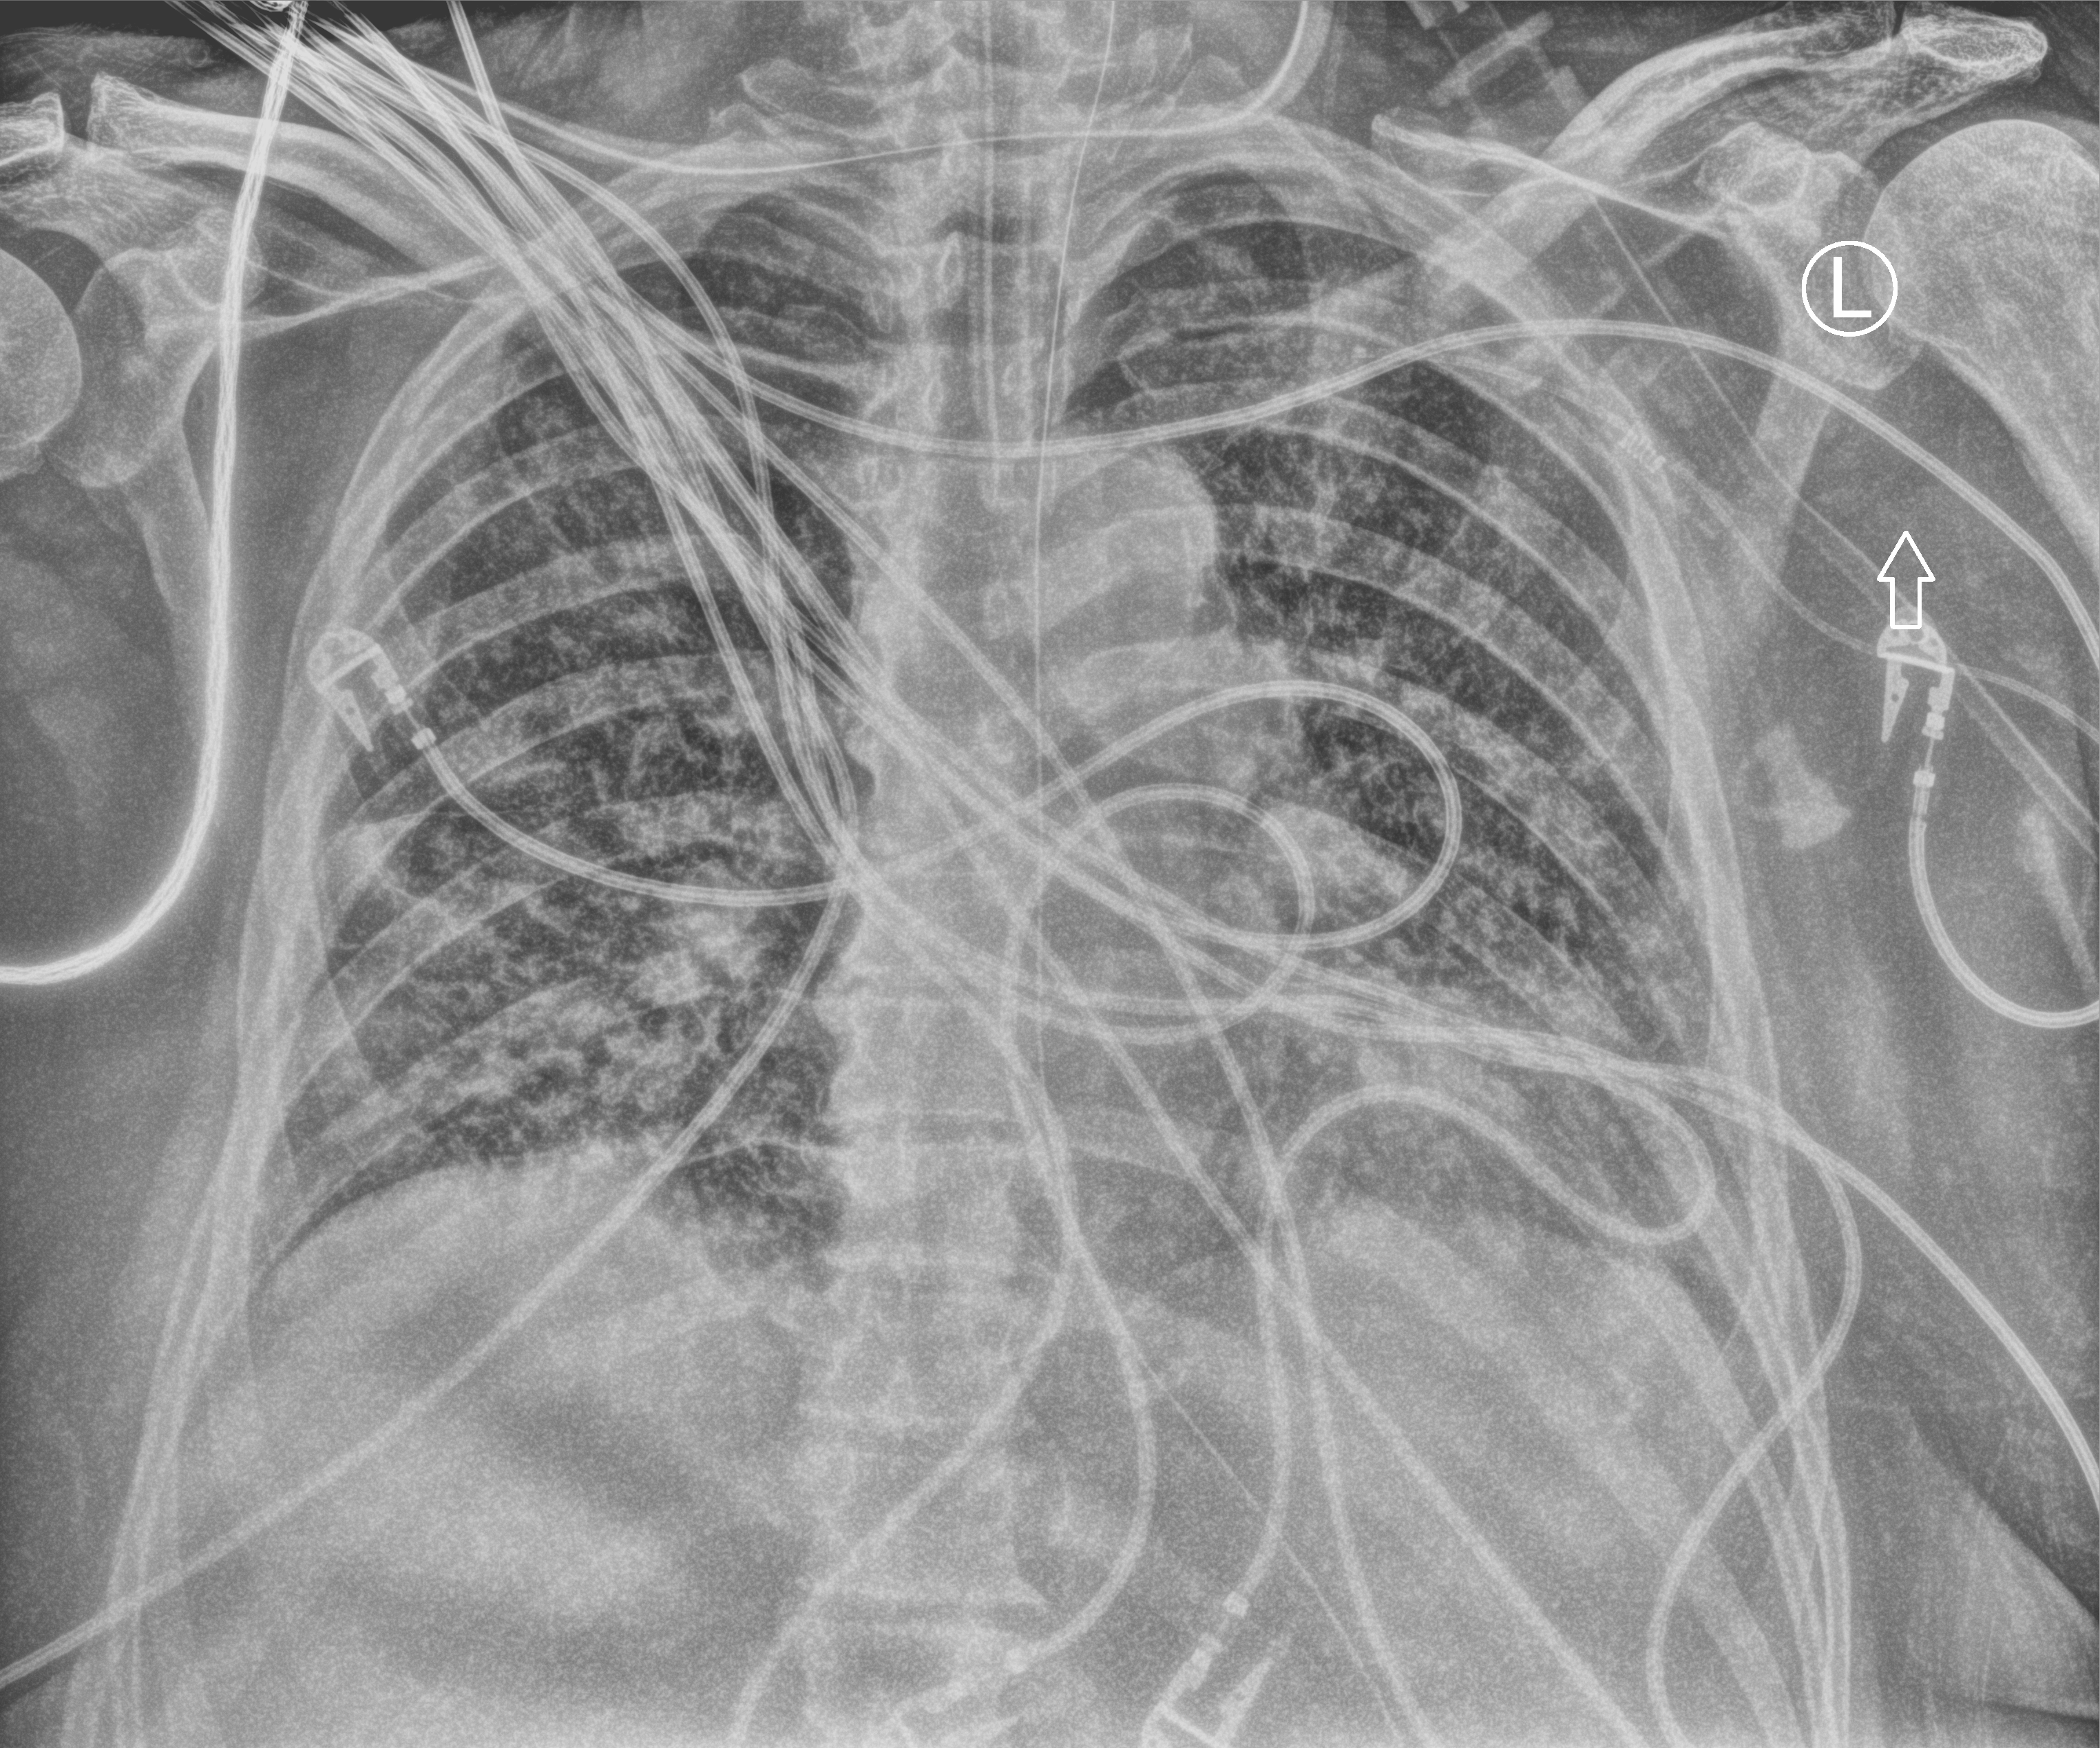
Portable chest radiograph; anteroposterior (AP) projection. Male patient hospitalised with COVID-19, age 60–74 years.
Admission-level facts for this patient (not findings on this image; timing relative to this image not recorded):
- smoking status (admission record): former
- mechanically ventilated during this hospital stay: yes
- COPD (admission record): no